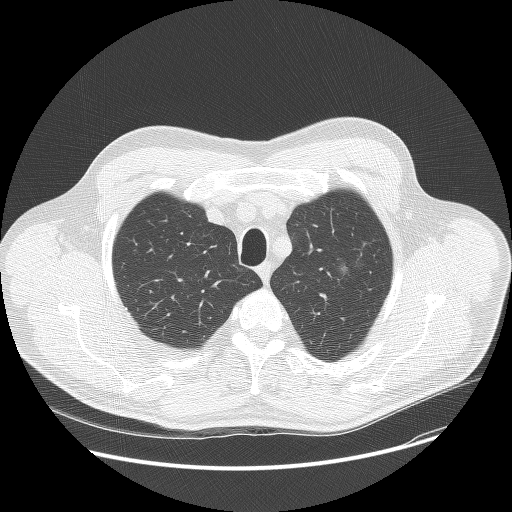
Chest CT (low-dose screening protocol), one axial image; first (baseline) screen; lung window (W 1500 / L -600 HU); 2.5 mm slice thickness. Male, age 60 years at enrolment. Former smoker at enrolment.
Lesion marked by an expert reader, box from (x=317, y=247) to (x=371, y=290) px. The screening reader recorded 2 non-calcified nodules or masses ≥4 mm on this exam (left upper lobe, right lower lobe); which of them this box marks is not recorded. Participant outcome: lung cancer diagnosed 784 days after this screen — bronchiolo-alveolar carcinoma, non-mucinous, left upper lobe, well differentiated (G1), stage IA (AJCC 6th edition), 16 mm at pathology.